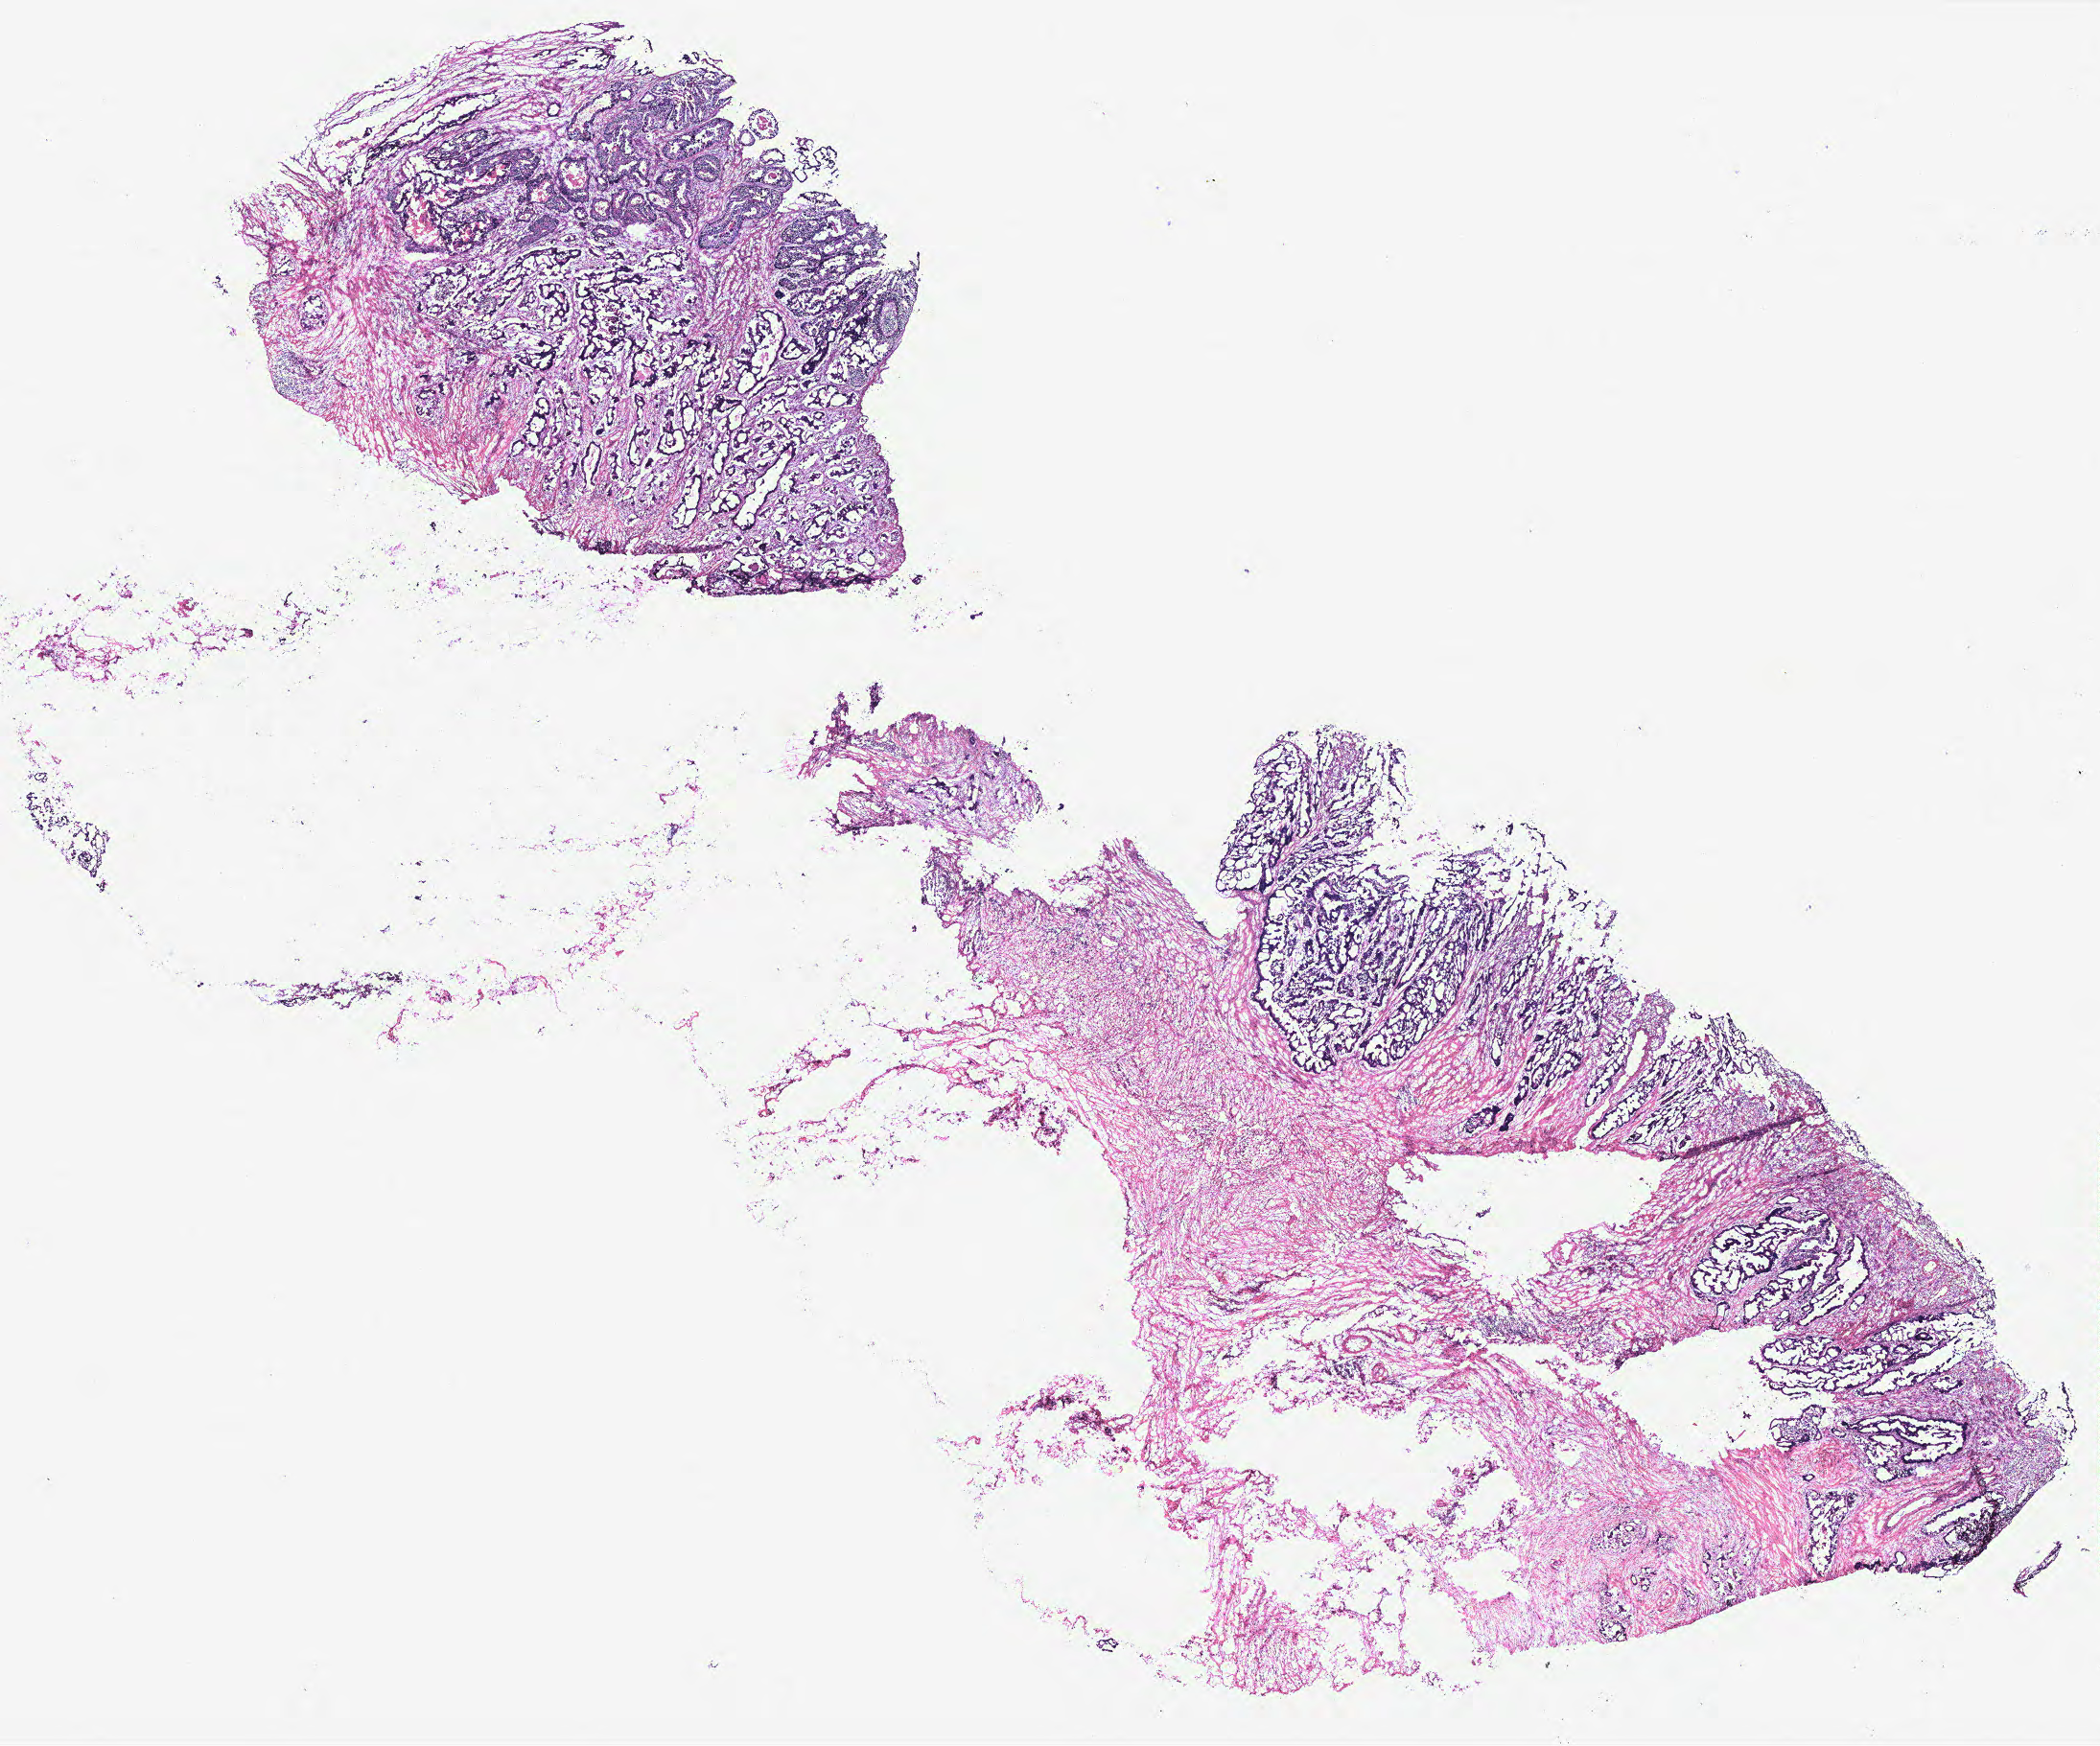
Hematoxylin and eosin (H&E) stained whole-slide image, a low-resolution overview of the entire scanned area, about 17.5 x 14.6 mm, colon, tissue type not recorded. Male patient.
Patient diagnosis: Adenocarcinoma, NOS.